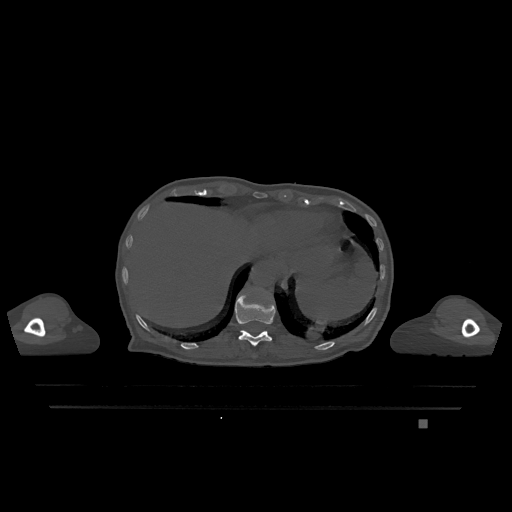
CT including the spine, one axial slice; position 583 of 1317 along the scan axis; bone window (W 1800 / L 400 HU); 0.5 mm slice thickness; 512 × 512 image matrix, field of view 500 × 500 mm. Female patient, age 74 years. Case-level facts recorded for this patient, not image findings: primary cancer: lung; vertebrae with lytic lesions (as recorded): T1, T4, T5, T6, L4, L5.
Annotated regions visible in this slice (semi-automatically segmented with operator editing):
- T11 vertebra: bounding box [x1, y1, x2, y2] px = [235, 293, 276, 346]